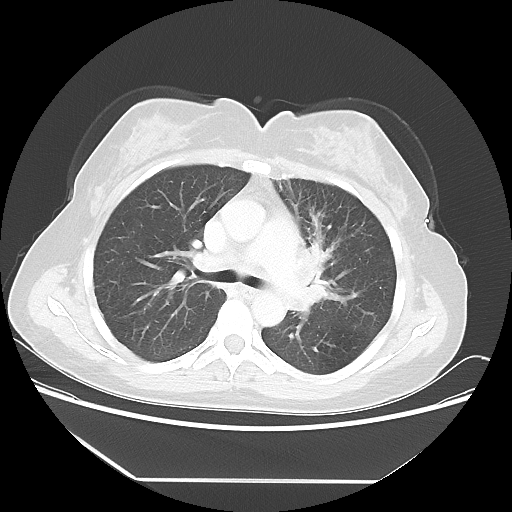
Chest CT, one axial slice. Position 33 of 52 along the scan axis. Reconstruction kernel LUNG. 100 kVp. Lung window (W 1500 / L -600 HU). 512 × 512 image matrix, field of view 390 × 390 mm. Patient: female, 50 years. From the clinical record (not read from this slice): clinical TNM (as recorded): T2 N3 M0.
Structures marked on this image (rectangle marked by the reading radiologist):
- lung tumour (recorded histology: adenocarcinoma): box from (x=289, y=236) to (x=345, y=324) px